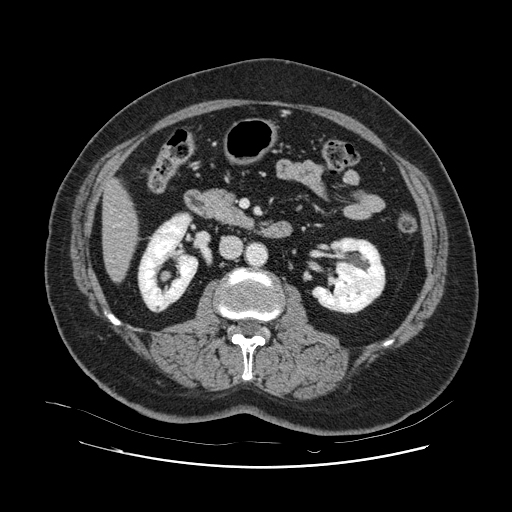
Contrast-enhanced abdominal CT, one axial slice; position 28 of 132 along the scan axis; intravenous contrast given; soft-tissue window (W 400 / L 40 HU); 2.5 mm slice thickness; 512 × 512 image matrix, field of view 391 × 391 mm. Female patient, age 73 years. From the clinical record (not read from this slice): diagnosis: colorectal cancer liver metastases, imaged before liver resection.
Annotated regions visible in this slice (manually delineated by an expert):
- hepatic veins: box from (x=113, y=225) to (x=119, y=227) px
- liver: (x=103, y=183)–(x=136, y=280)
- planned liver remnant (the part of the liver to remain after resection): (x=104, y=183)–(x=137, y=280)